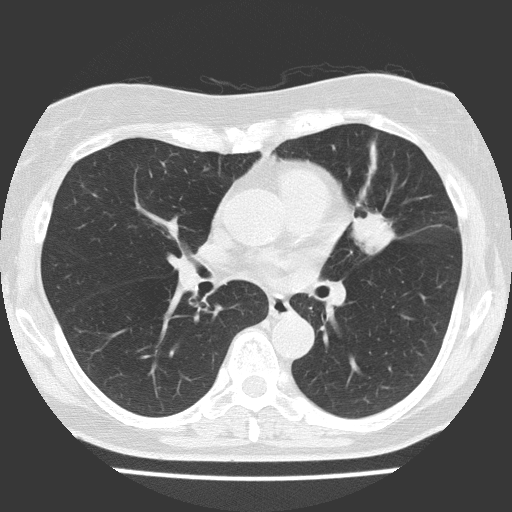
Low-dose screening chest CT, axial slice, first (baseline) screen, lung window (W 1500 / L -600 HU), 2 mm slice thickness, lung (sharp) reconstruction kernel (FC51), slice 73 of 151 in the series. Female participant, aged 70 years at enrolment.
Lesion marked by an expert reader, box from (x=321, y=179) to (x=432, y=274) px. The screening reader recorded 2 non-calcified nodules or masses ≥4 mm on this exam (left upper lobe, right upper lobe); which of them this box marks is not recorded. Official screen result: positive, change unspecified: nodule(s) >= 4 mm or enlarging nodule(s), mass(es), or other non-specific abnormalities suspicious for lung cancer. Later outcome: lung cancer diagnosed 25 days after this screen — adenocarcinoma, NOS, left upper lobe, poorly differentiated (G3), stage IV (AJCC 6th edition), 30 mm at pathology.